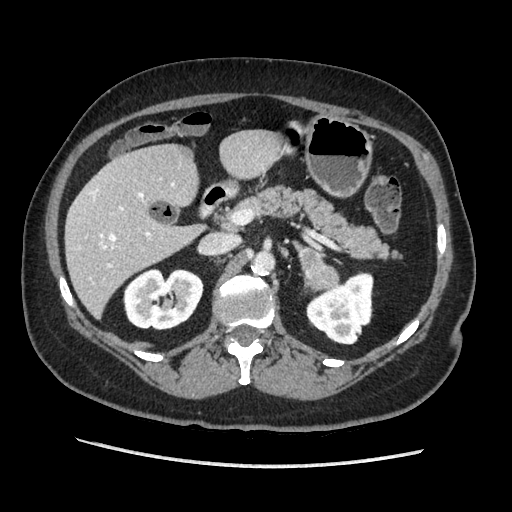
Contrast-enhanced abdominal CT, one axial slice; position 112 of 203 along the scan axis; soft-tissue window (W 400 / L 40 HU); 1.25 mm slice thickness; 512 × 512 image matrix, field of view 360 × 360 mm. Female patient. From the clinical record (not read from this slice): diagnosis: adrenocortical carcinoma; tumour side: left adrenal; tumour size at pathology: 6.5 cm; Ki-67 index: 22 %; stage (as recorded): 2.
Annotated regions visible in this slice (semi-automatically segmented with operator editing):
- mass: box from (x=300, y=248) to (x=339, y=288) px